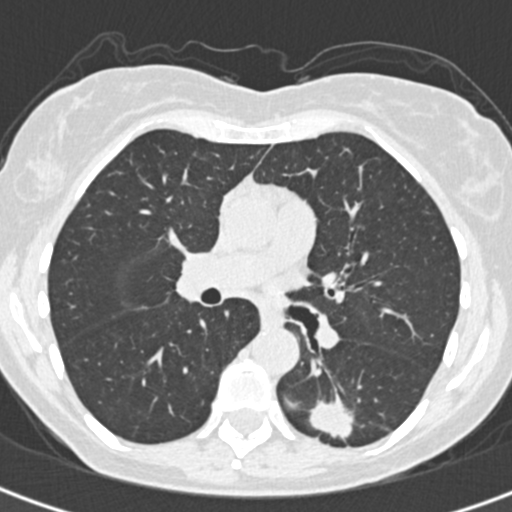
Low-dose screening chest CT, one axial slice; slice 194 of 328 in the series (ordered by position); reconstruction kernel B30f; 120 kVp; lung window (W 1500 / L -600 HU); 1 mm slice thickness; 512 × 512 image matrix, field of view 284 × 284 mm.
Annotated regions visible in this slice (manually delineated by an expert):
- lesion 1 (tumor, lower lobe of left lung): box from (x=309, y=398) to (x=354, y=439) px